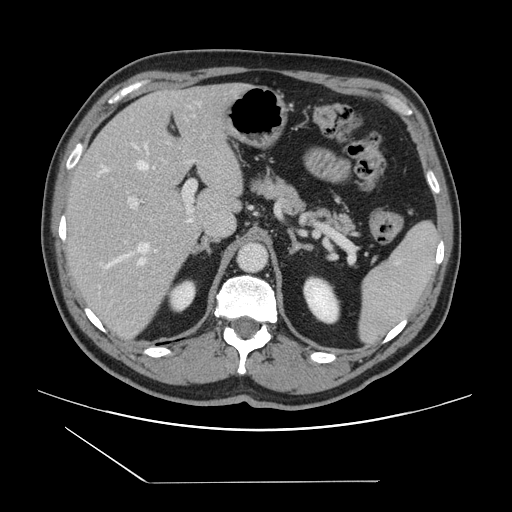
Contrast-enhanced abdominal CT, one axial slice. Slice 92 of 157 in the series (ordered by position). 120 kVp. Intravenous contrast given. Soft-tissue window (W 400 / L 40 HU). 512 × 512 image matrix, field of view 407 × 407 mm. Male patient, age 61 years. Case-level facts recorded for this patient, not image findings: diagnosis: colorectal cancer liver metastases, imaged before liver resection.
Structures marked on this image (outlined manually by an expert reader):
- hepatic veins: bounding box <100,144,153,268> (left, top, right, bottom; pixels)
- liver: <64,85,243,338>
- planned liver remnant (the part of the liver to remain after resection): <67,85,237,223>
- portal vein (with intrahepatic branches): <128,180,196,222>